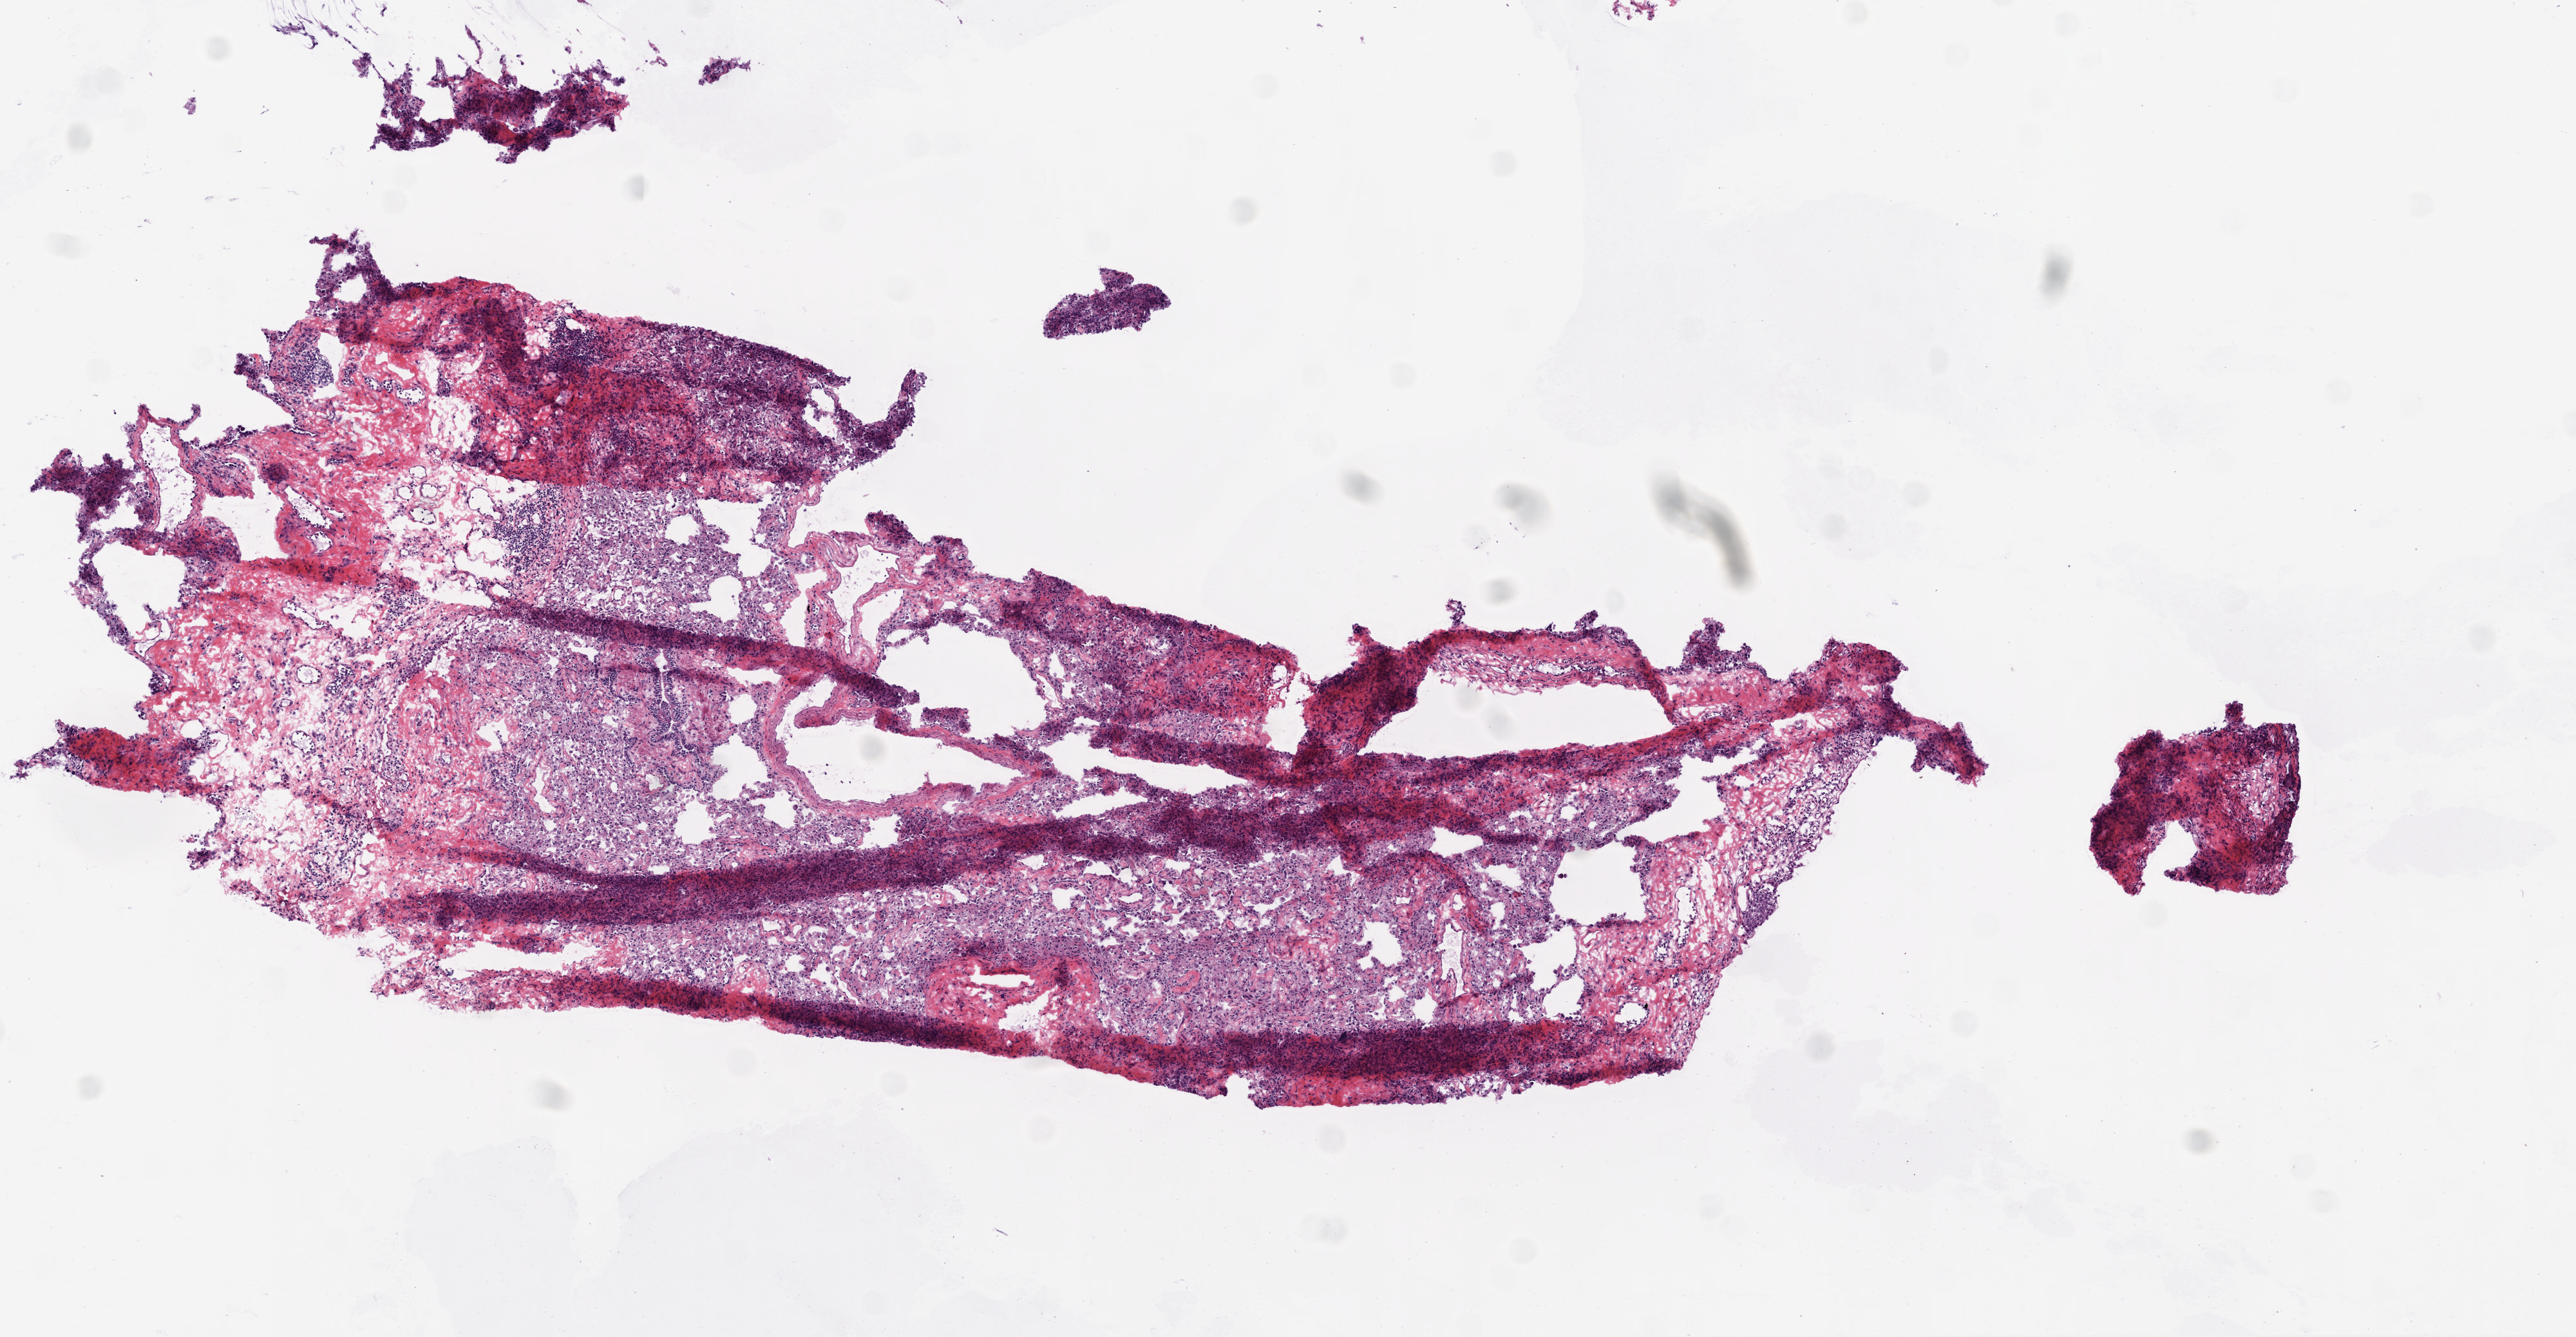
Digitized Hematoxylin and eosin (H&E) stained tissue section (whole slide), whole scanned area (about 8.0 x 4.2 mm) shown as a low-resolution overview; frozen section from the bottom of the tissue portion; lung, solid tissue normal (non-tumour tissue) sample. Male, age 56 years at initial diagnosis.
This section: solid tissue normal (non-tumour) sample from the same patient. Patient diagnosis: Squamous cell carcinoma, NOS (lower lobe, lung).